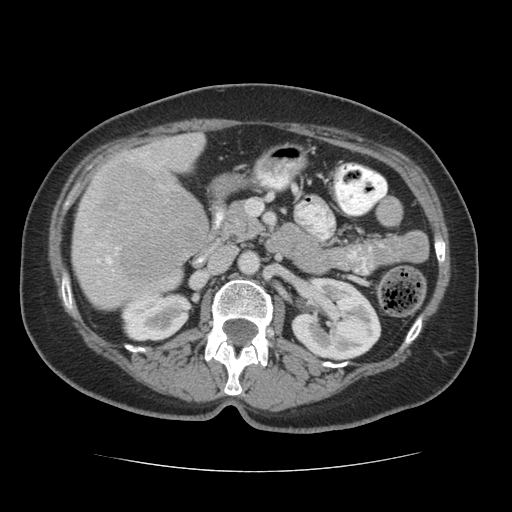
Contrast-enhanced abdominal CT (liver protocol), one axial slice. Position 21 of 75 along the scan axis. 140 kVp. Soft-tissue window (W 400 / L 40 HU). 2.5 mm slice thickness. 512 × 512 image matrix, field of view 360 × 360 mm. Case-level facts recorded for this patient, not image findings: diagnosis: hepatocellular carcinoma (patient treated with transarterial chemoembolisation; whether this scan precedes or follows treatment is not stated here); TNM stage (as recorded): Stage-I; Child-Pugh class: A; tumour differentiation: moderately differentiated; tumour nodularity: uninodular.
Structures marked on this image (semi-automatically segmented with operator editing):
- liver parenchyma outside the tumour (the mass and vessels are separate outlines, so this box may not span the whole liver): bounding box <72,132,210,308> (left, top, right, bottom; pixels)
- mass: <89,158,207,288>
- liver vessels: <84,153,144,272>